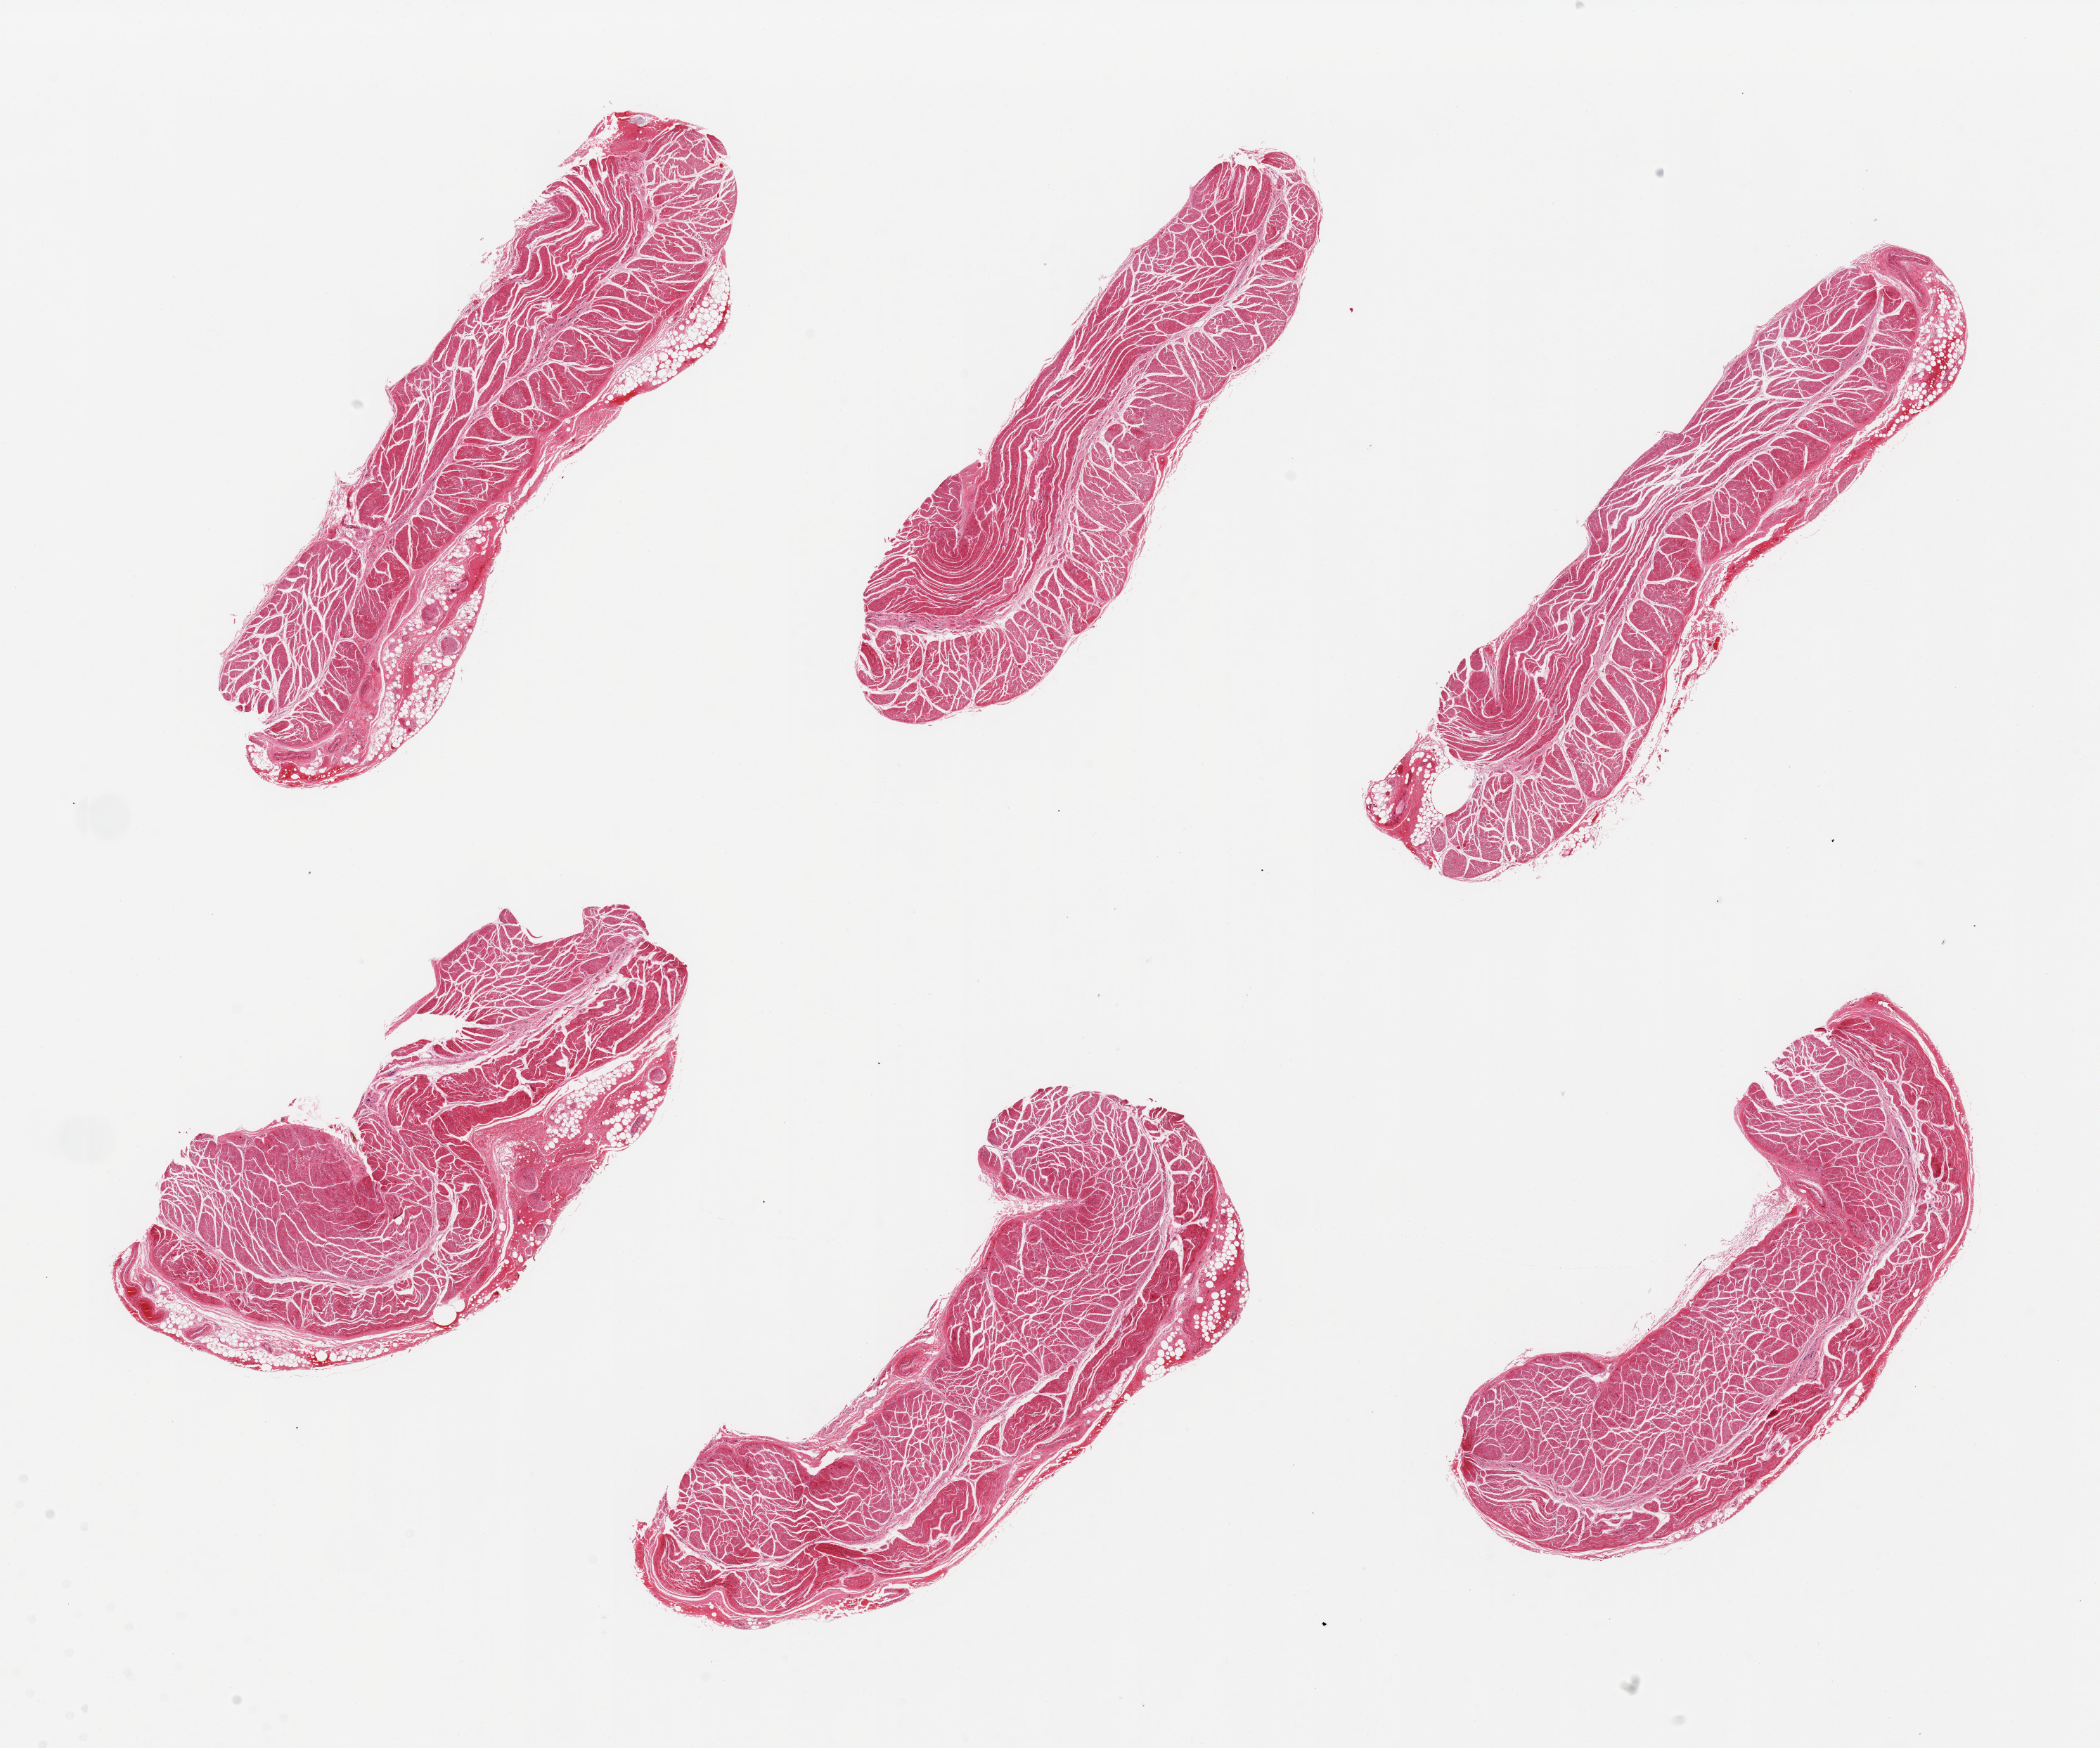
H&E whole-slide image, low-resolution overview of the scanned area, about 23.6 x 19.7 mm (slide scanned at 20x), PAXgene-fixed paraffin-embedded (PFPE) section, sampled site (target tissue): esophageal muscle, tissue donor sample. Male donor.
* review note (as recorded): 6 pieces, all muscularis, good specimens